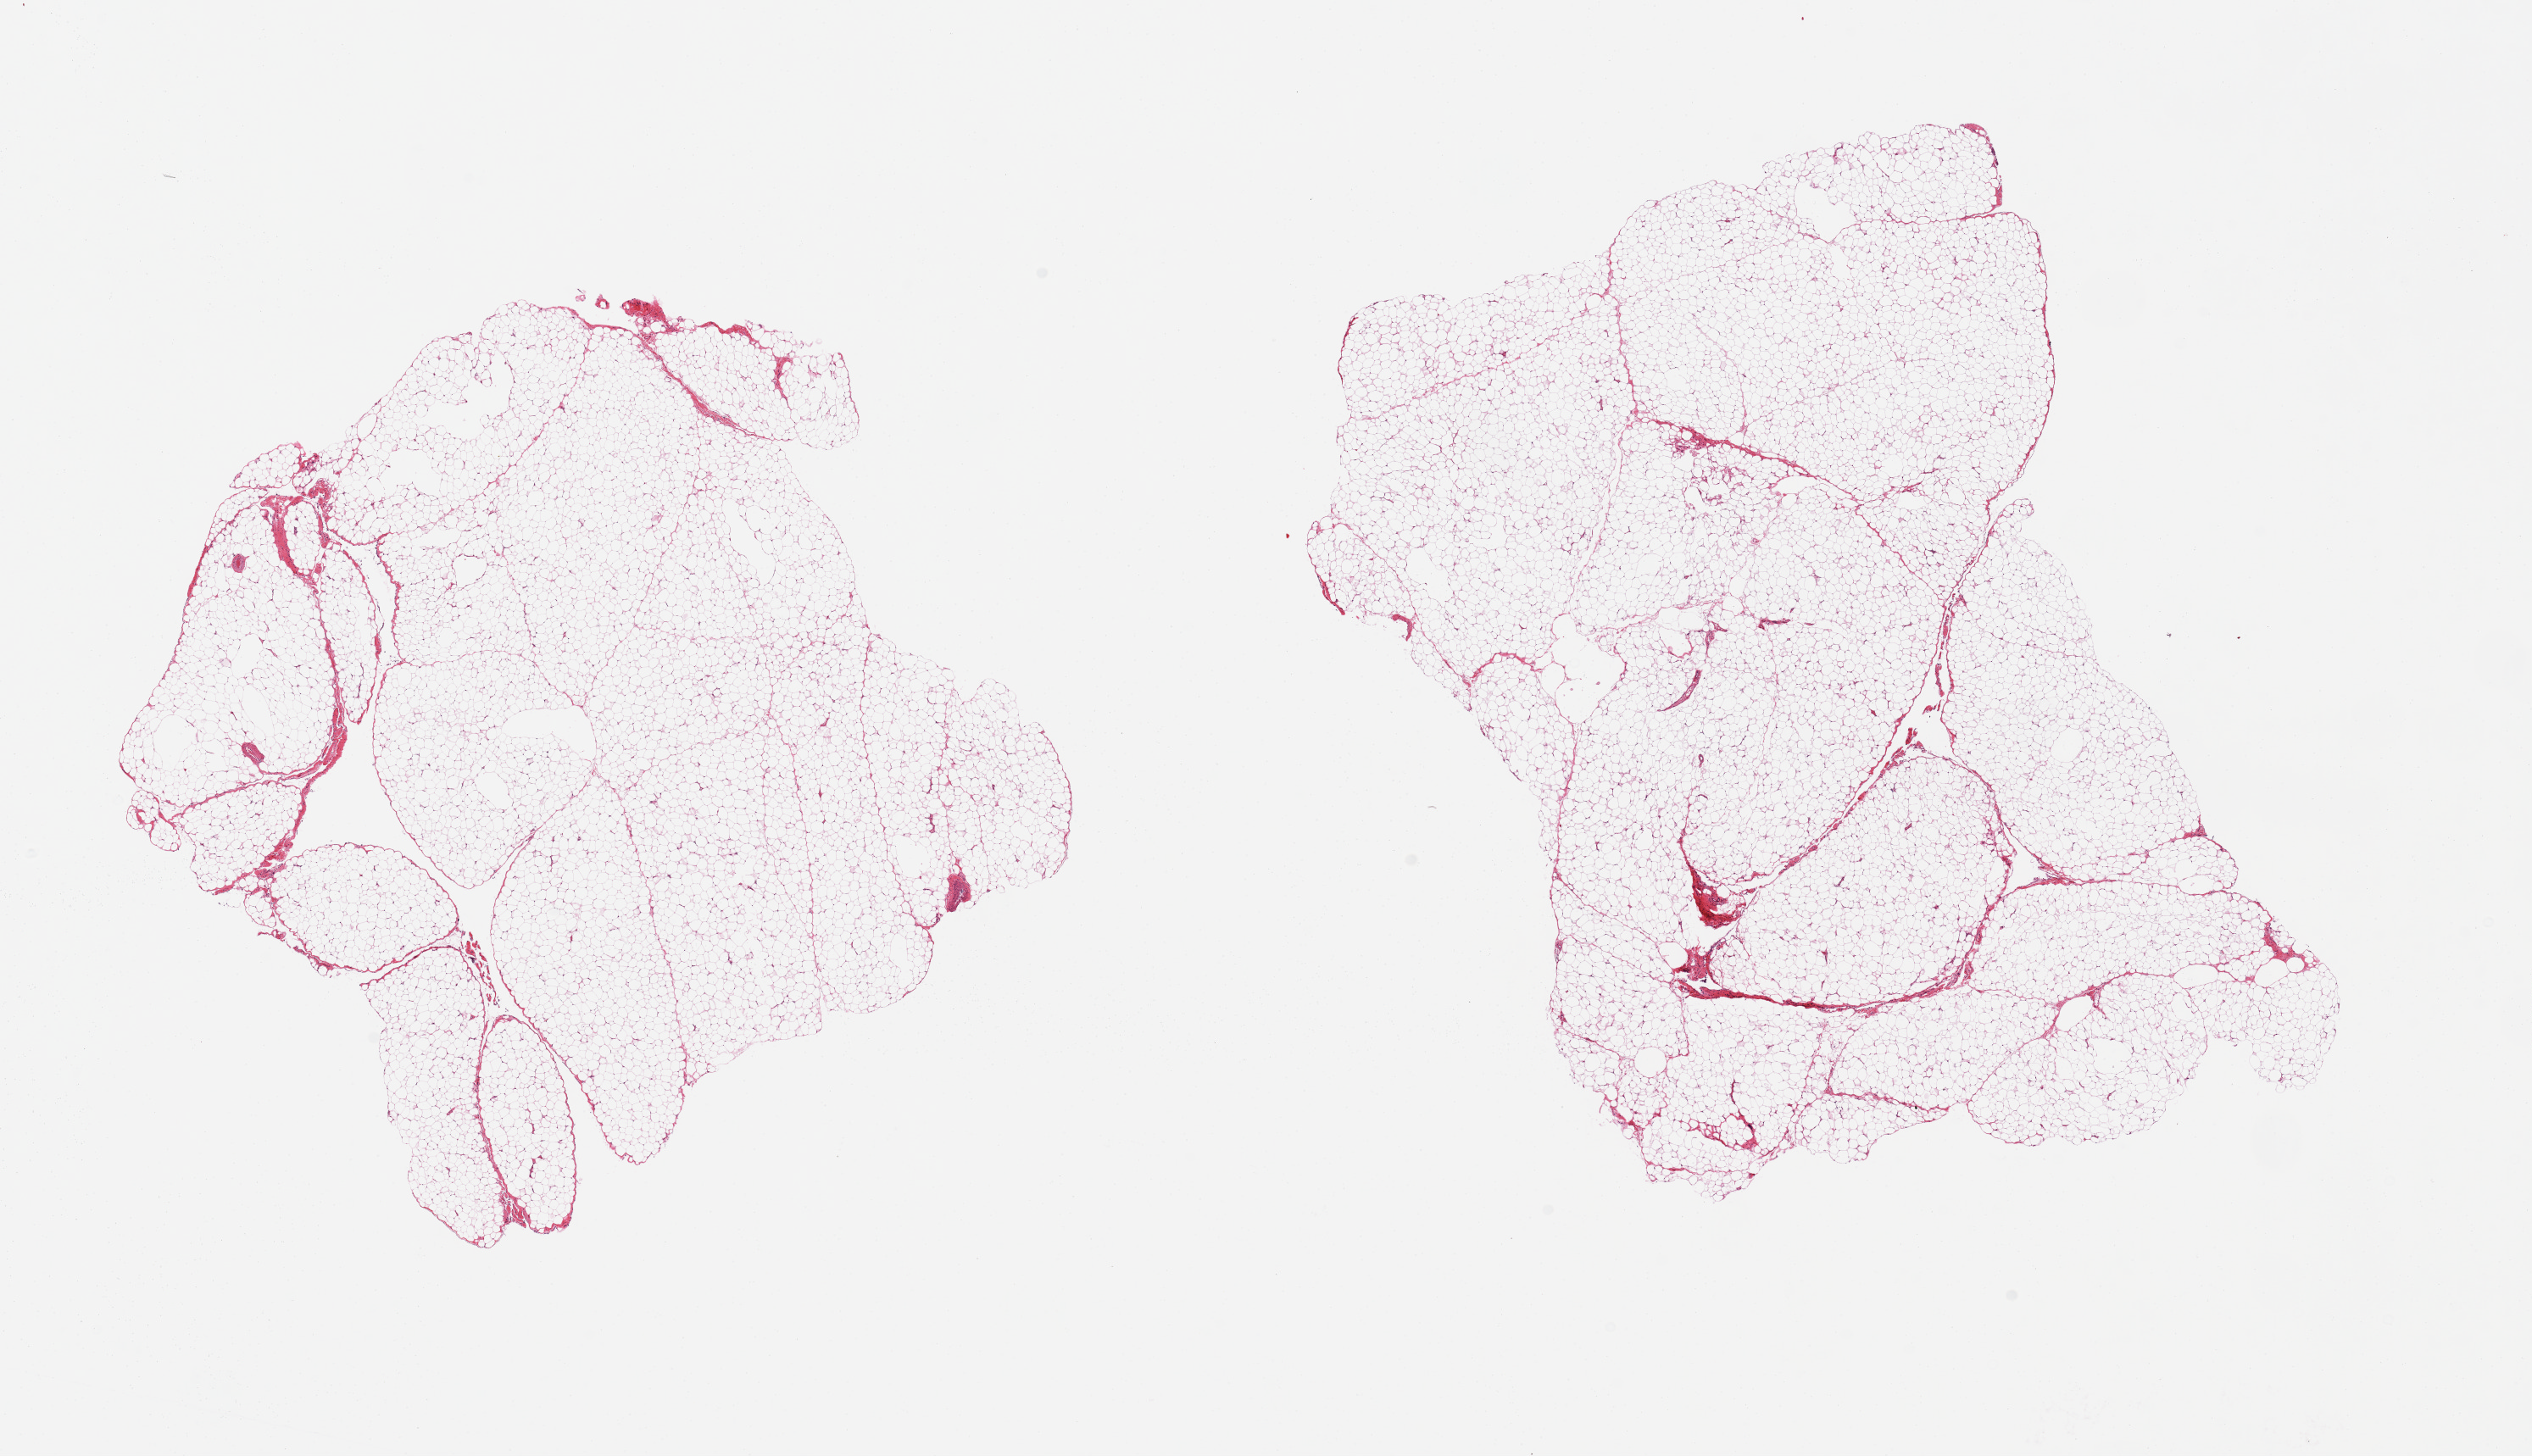
Whole-slide image, H&E stain — a low-resolution overview of the entire scanned area, about 23.6 x 13.6 mm; PAXgene-fixed paraffin-embedded (PFPE) section; section of omentum (target tissue); tissue donor sample. Female donor.
Pathologist's review note for this sample: 2 pieces, minimal fibrous tissue.